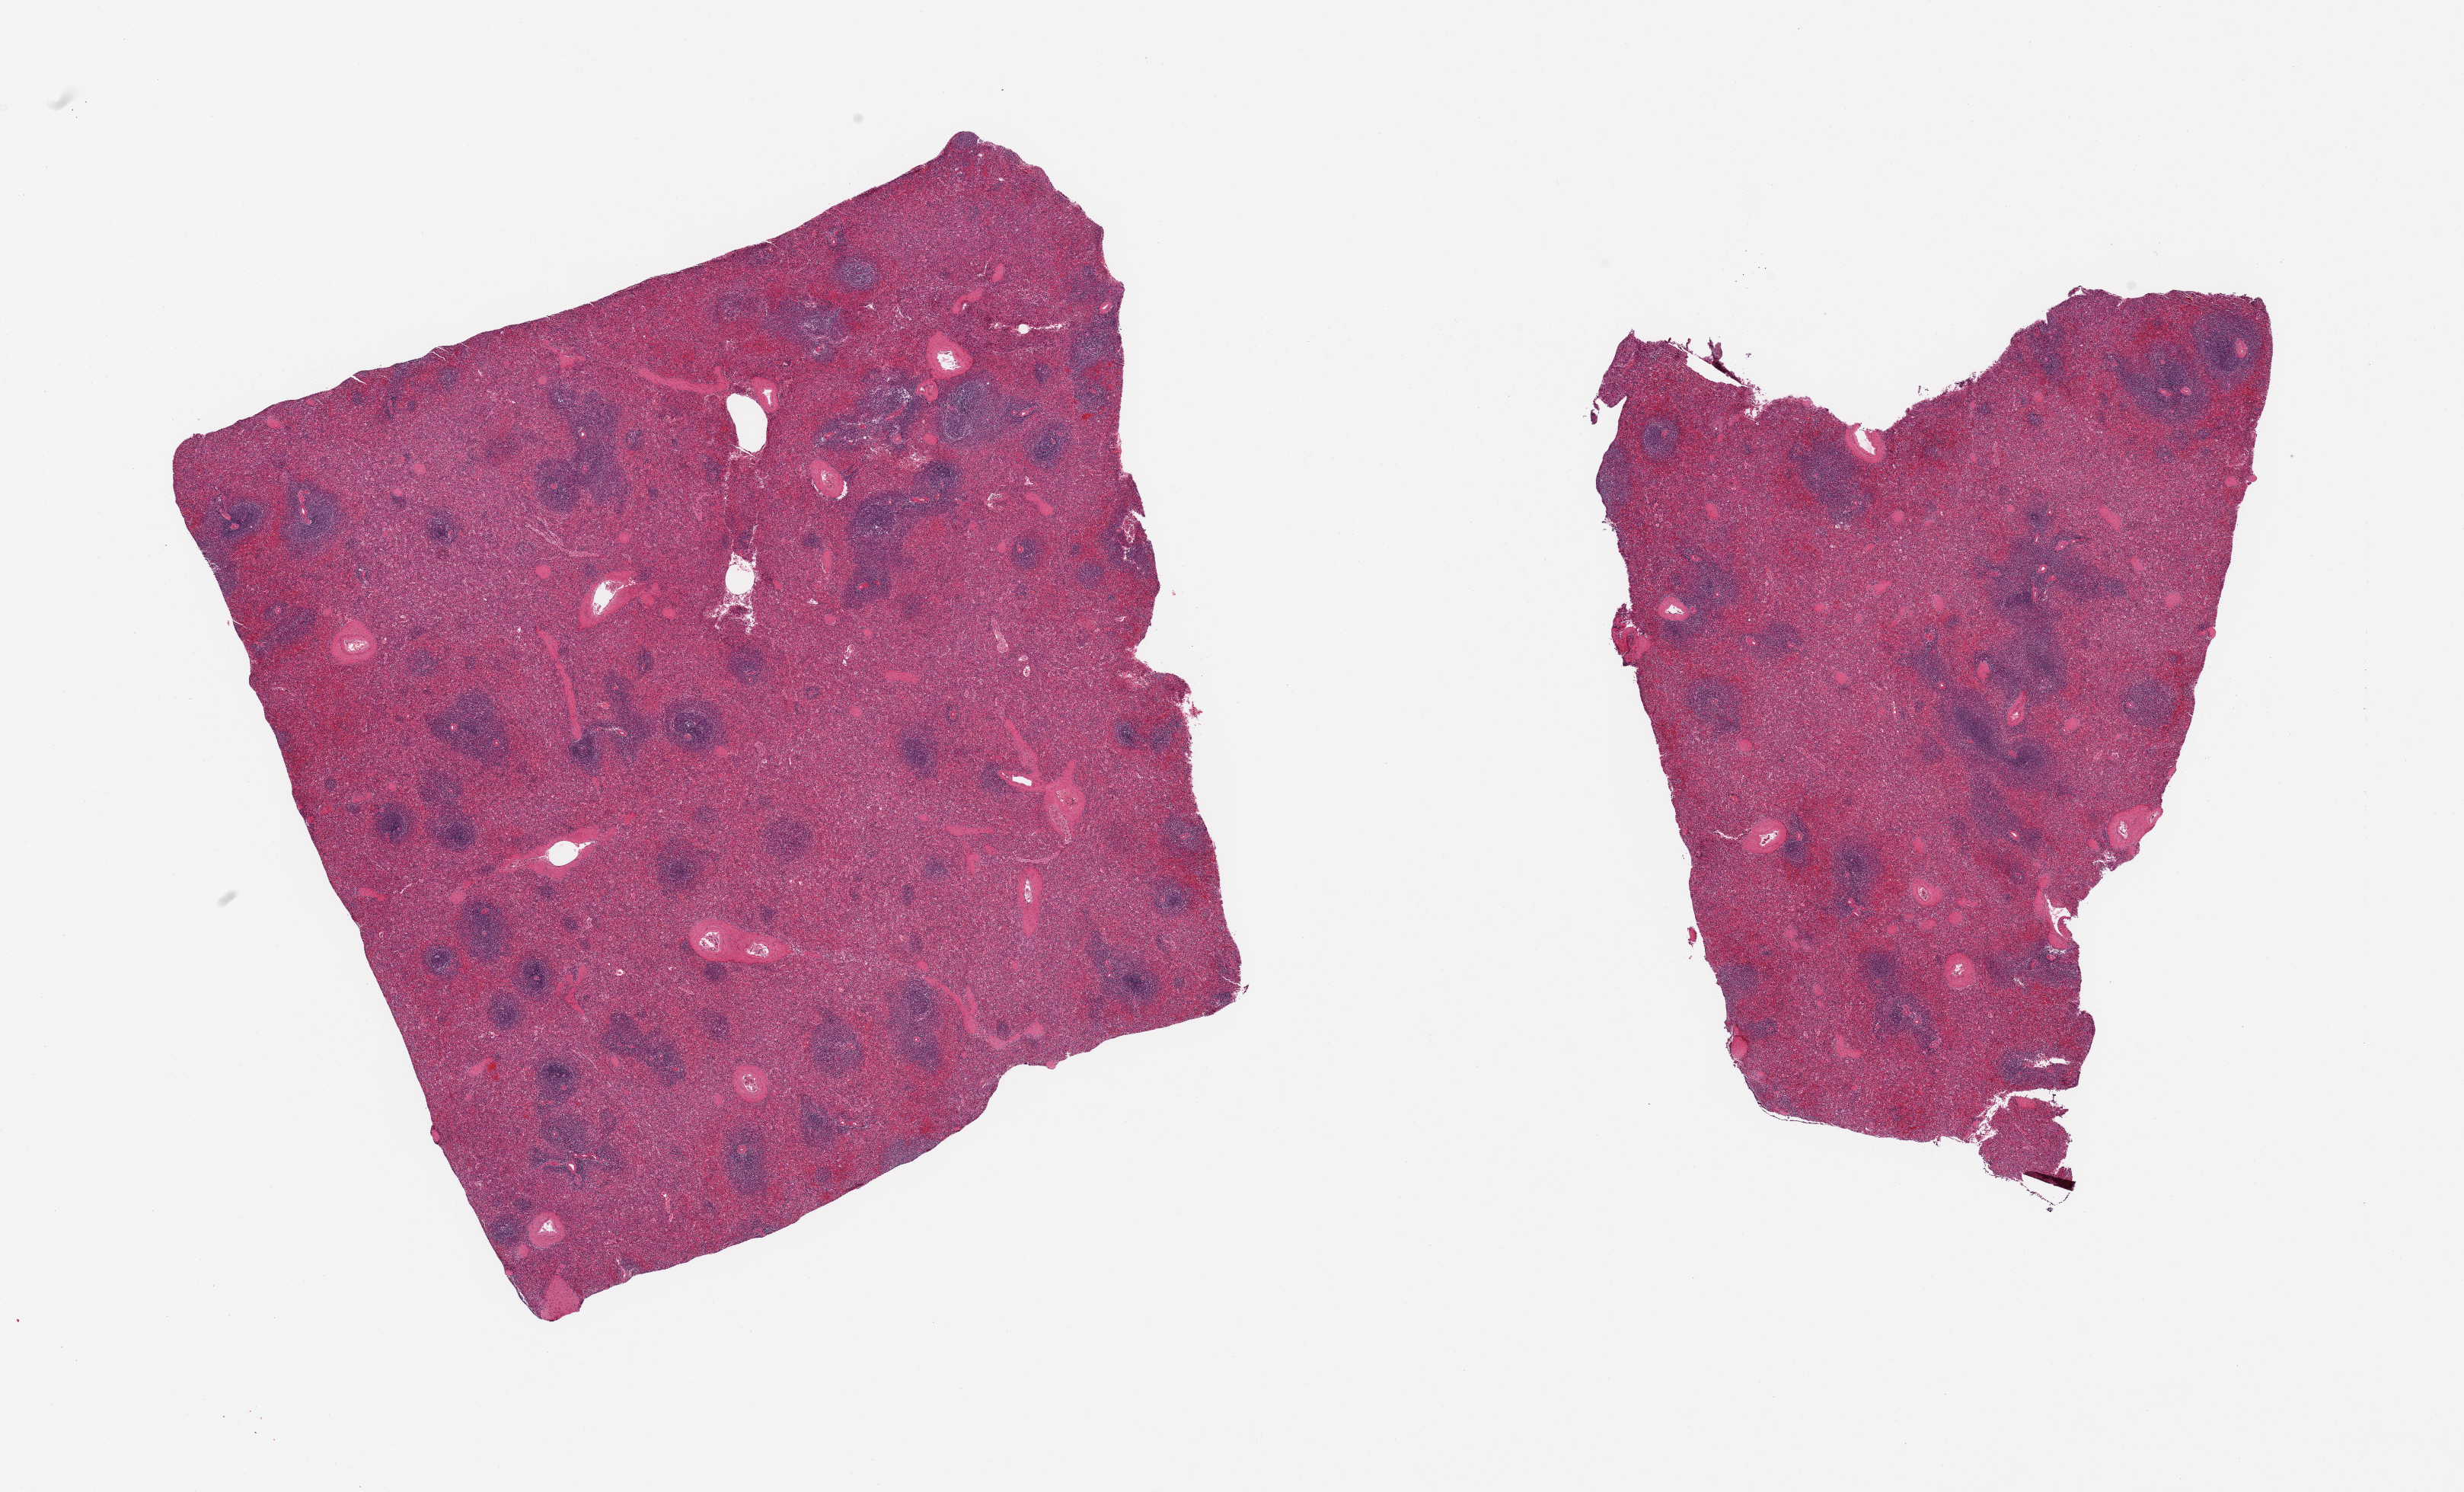
Digitized H&E-stained section, brightfield, whole scanned area (about 25.6 x 15.5 mm, from a 20x scan) shown as a low-resolution overview; PAXgene-fixed paraffin-embedded (PFPE) section; target tissue: spleen; donor tissue sample. Donor sex: male.
- pathologist's review note for this sample: 2 pieces, no abnormalities